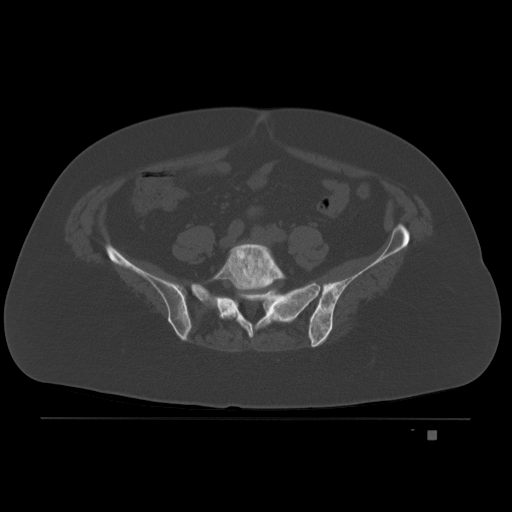
CT including the spine, one axial slice; position 28 of 221 along the scan axis; bone window (W 1800 / L 400 HU); 3 mm slice thickness; 512 × 512 image matrix. Patient: female, 63 years. From the clinical record (not read from this slice): primary cancer: breast.
Annotated regions visible in this slice (semi-automatically segmented with operator editing):
- L5 vertebra: bounding box <211,243,287,317> (left, top, right, bottom; pixels)